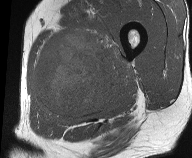
MRI of an extremity soft-tissue mass, one axial slice. Position 24 of 61 along the scan axis. MR volume resampled by the dataset authors to the PET/CT grid (not the native acquisition matrix). 3.27 mm slice thickness. 192 × 158 image matrix, field of view 187 × 154 mm. Male patient. Case-level facts recorded for this patient, not image findings: histological type: pleiomorphic liposarcoma; grade: high; site of the primary tumour: left thigh.
Annotated regions visible in this slice (expert contour drawn on MRI and transferred to this co-registered scan by the dataset authors):
- gross tumour volume including surrounding oedema: box from (x=32, y=28) to (x=131, y=122) px
- gross tumour volume (mass): (x=36, y=32)–(x=115, y=115)